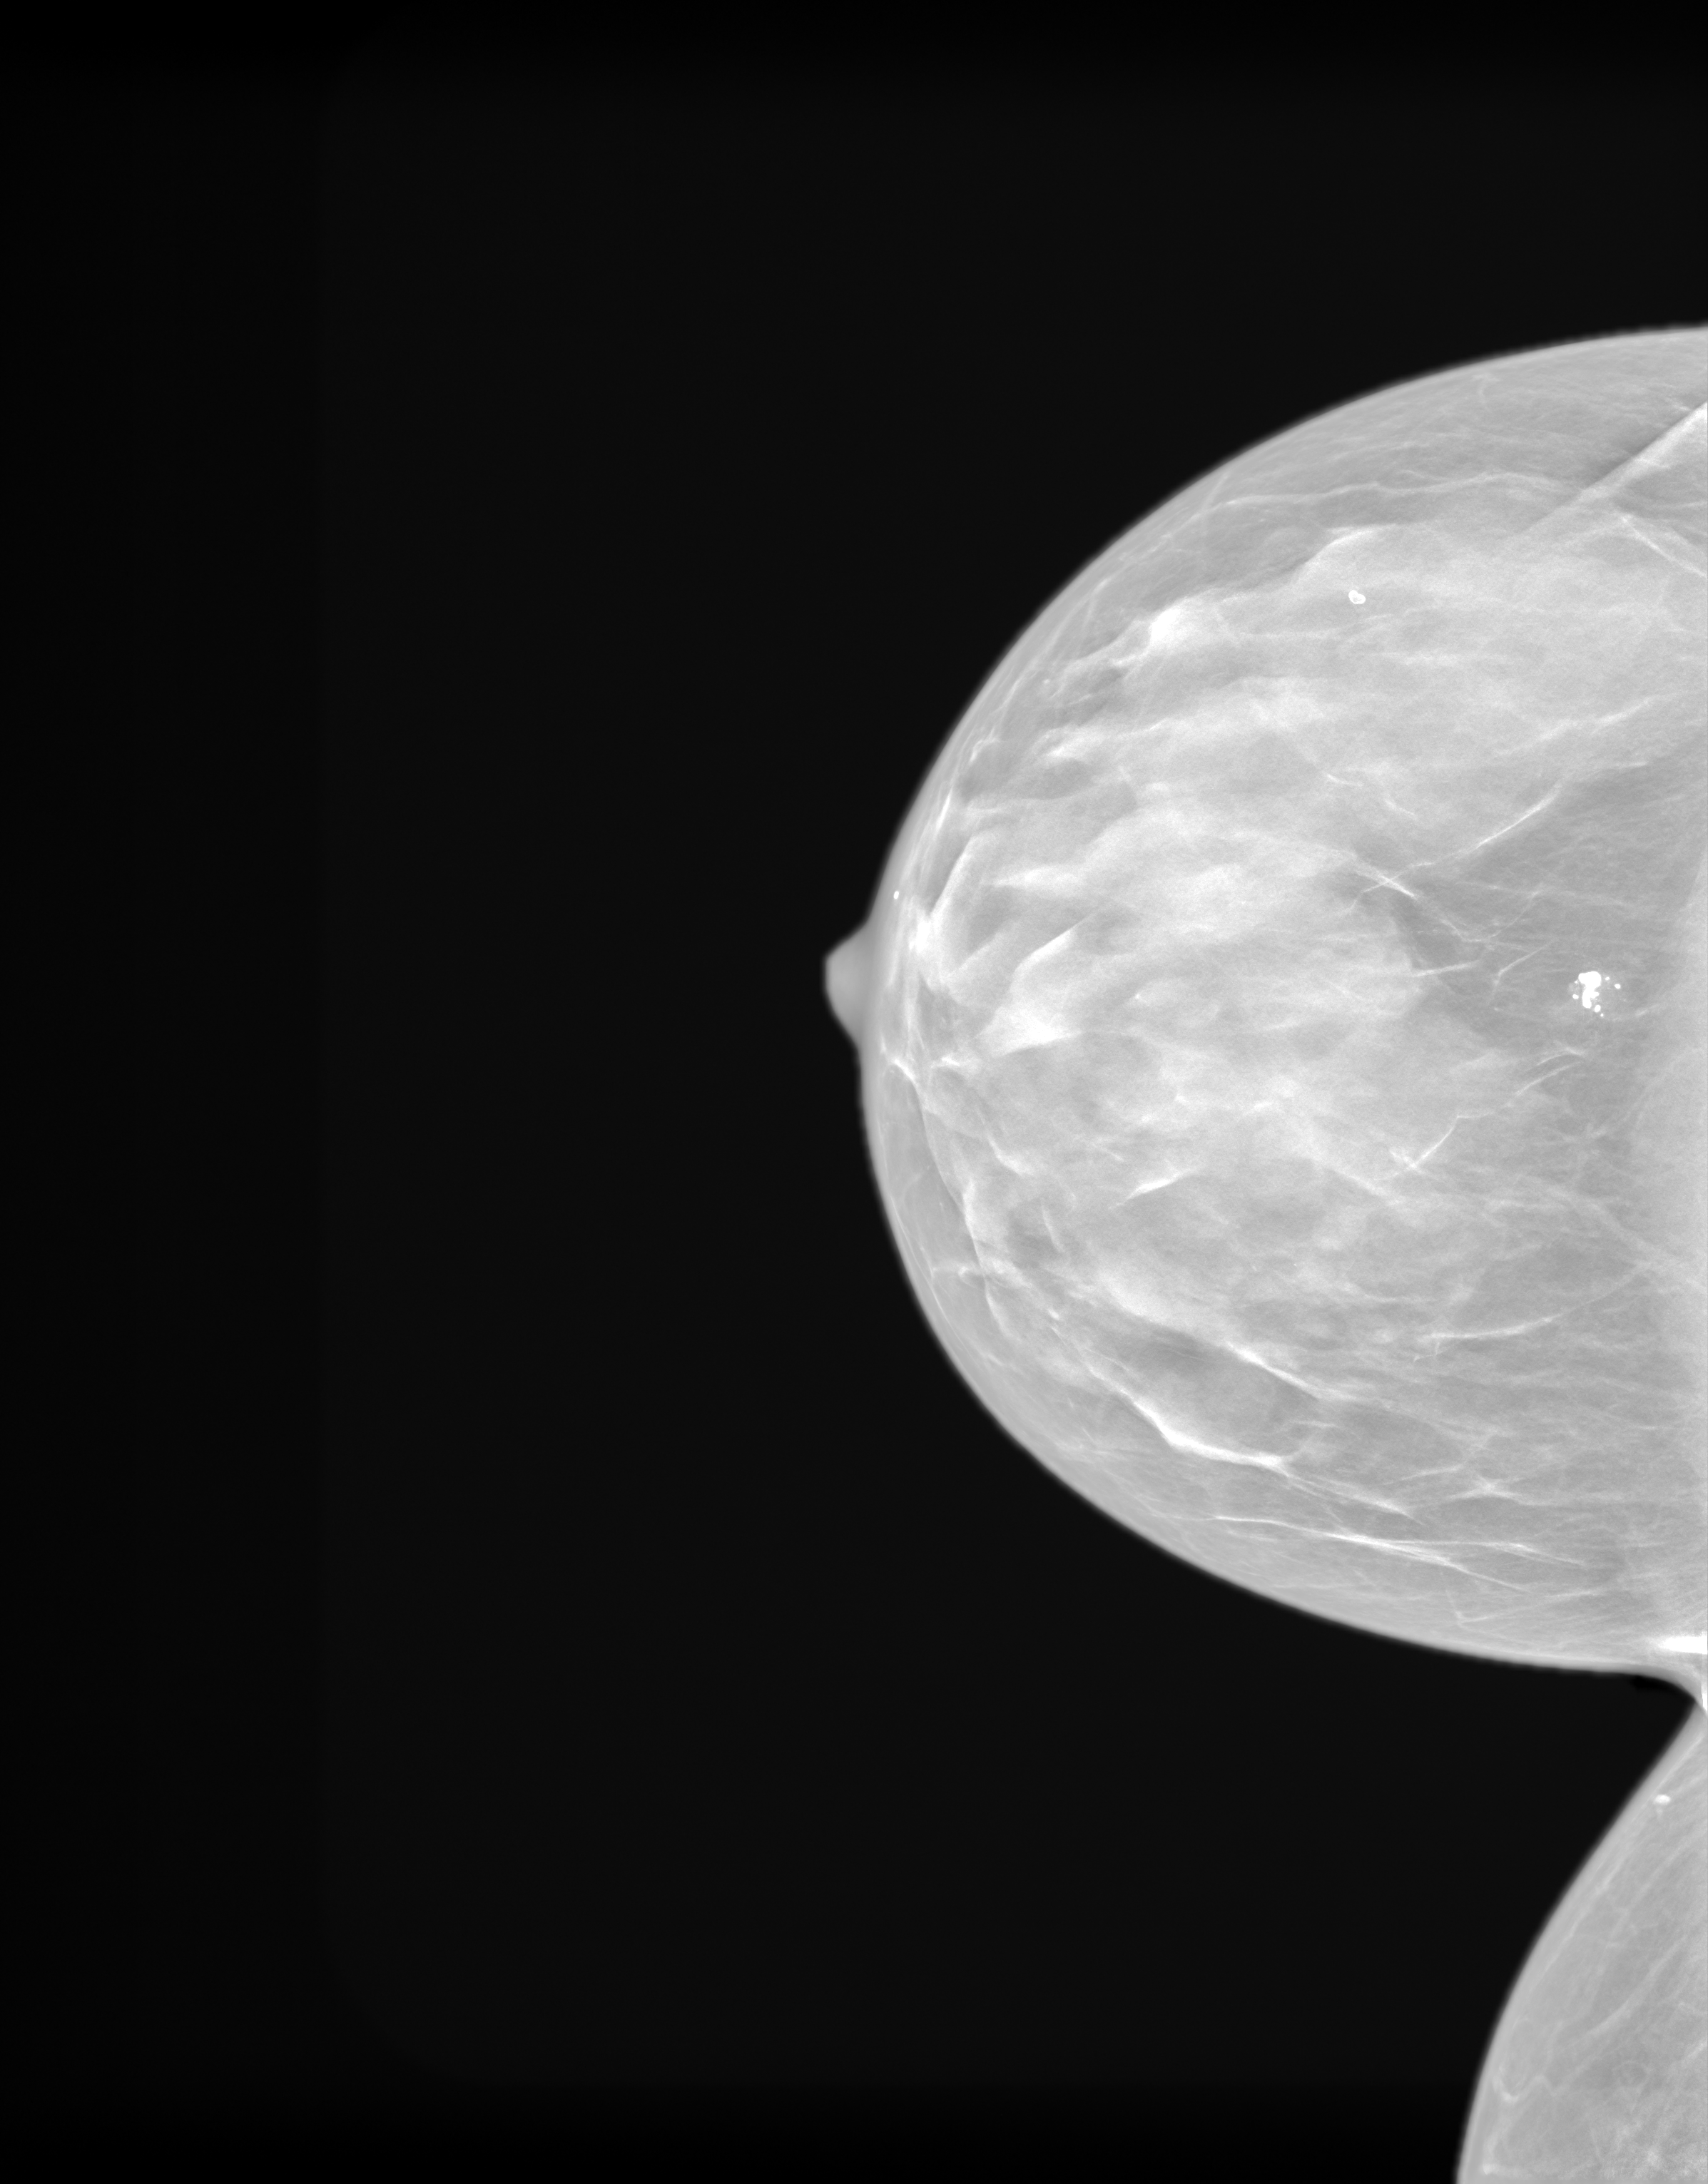
Synthetic 2-D view generated from a tomosynthesis acquisition (not an FFDM exposure); right breast; craniocaudal (CC) view; annual screening mammography examination; system: SenoIris_1SP1.1(421). Patient aged 60 years (female).
- BI-RADS breast density category at the screening exam (both breasts, scale 1–4): 4
- final BI-RADS category for the screening round (tomosynthesis exam, both breasts): category 1
- recall: no recall after this screen